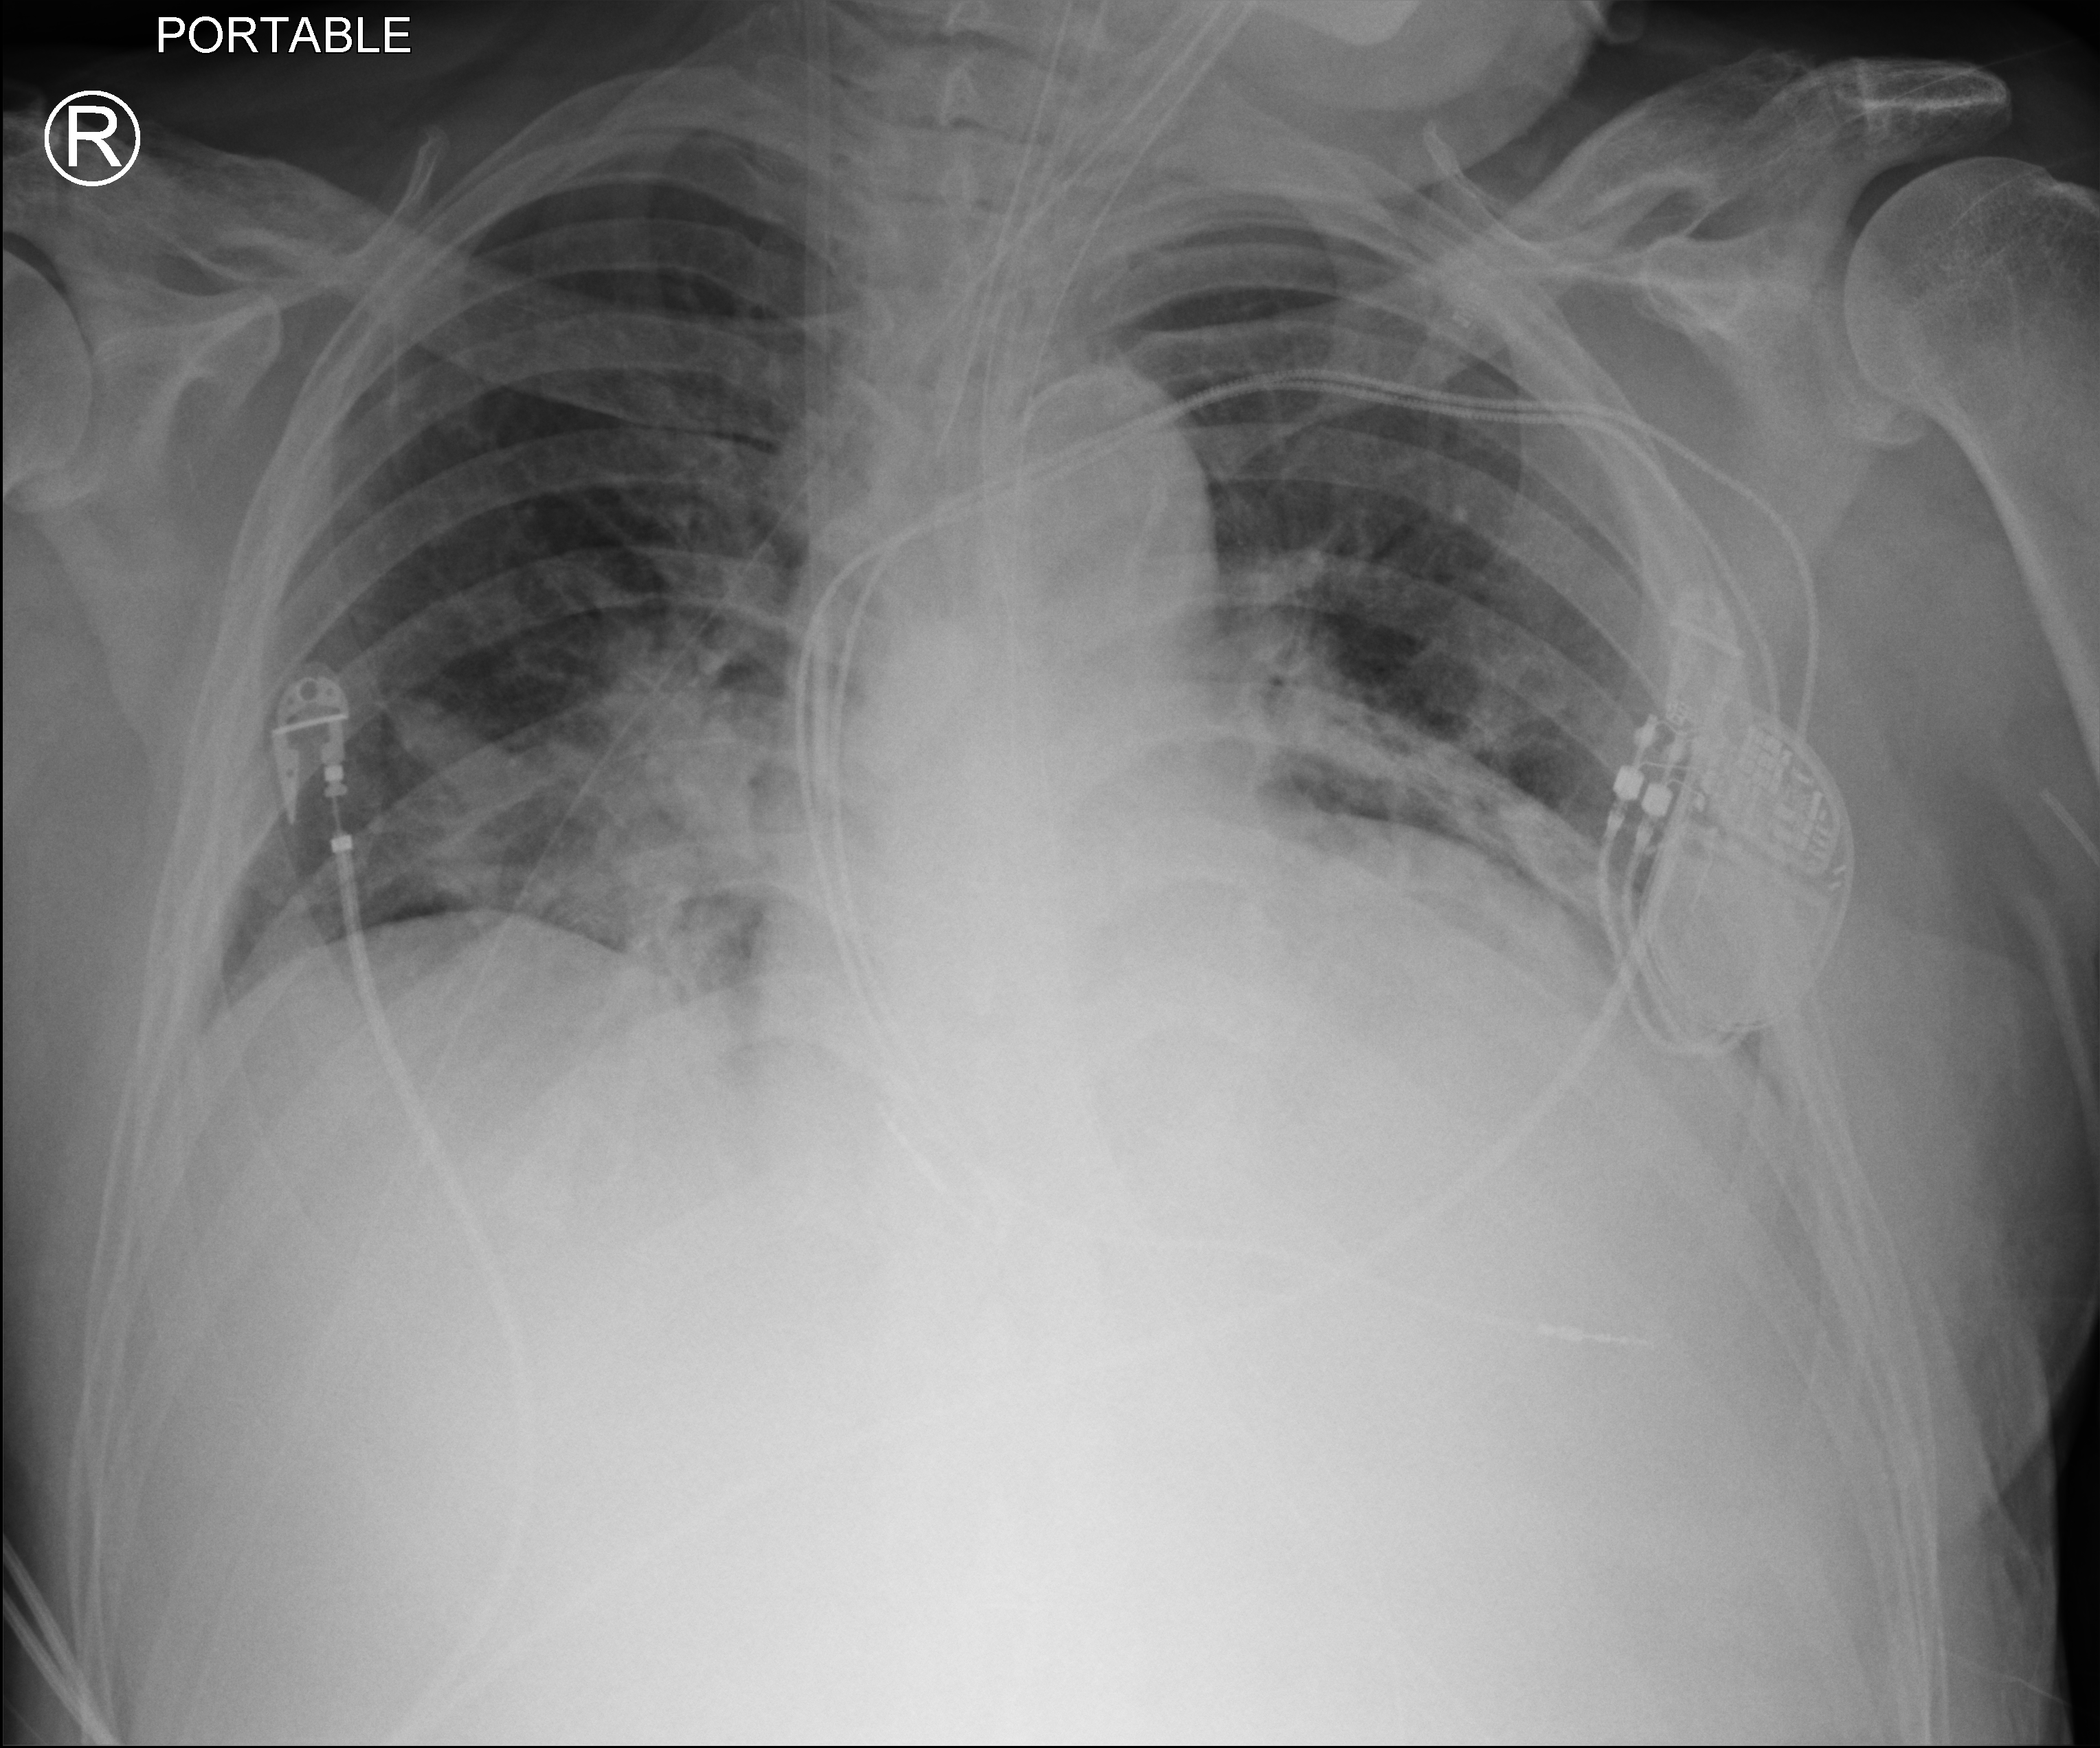
Portable chest radiograph, anteroposterior (AP) projection. Male patient hospitalised with COVID-19, age 60–74 years.
Hospital-stay facts (about this admission, not read from this image; timing relative to this image not recorded):
- mechanically ventilated during this hospital stay: yes
- length of hospital stay: 41 days